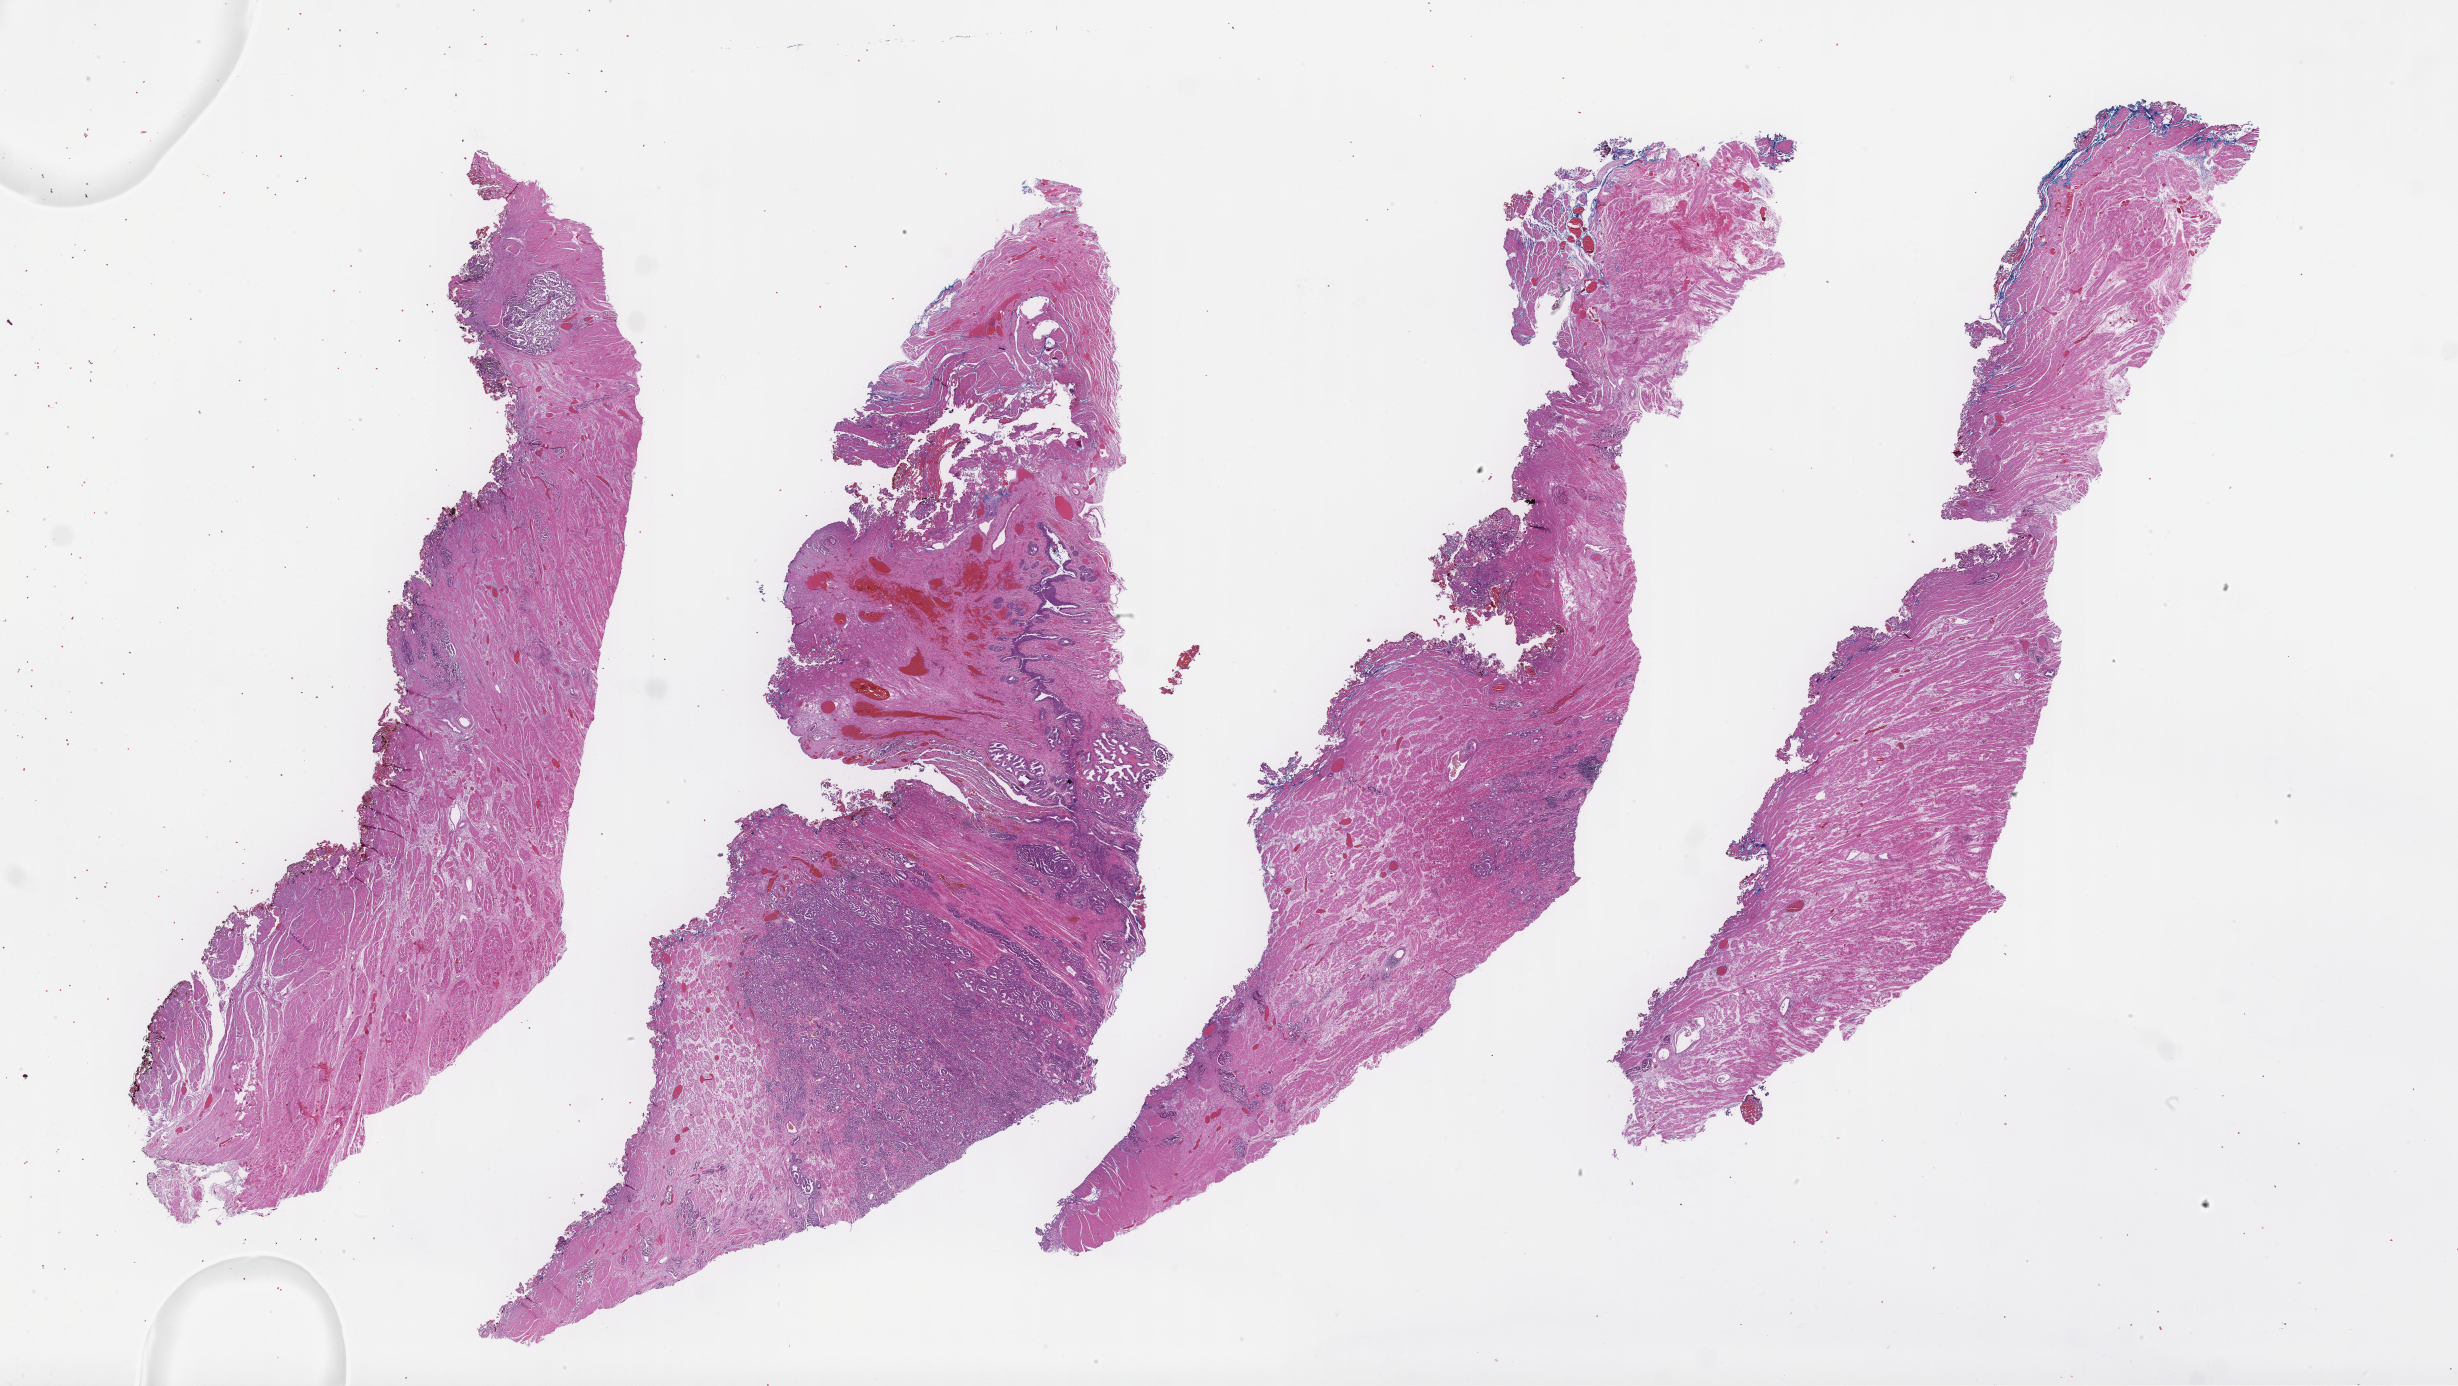
Digitized hematoxylin and eosin (H&E)-stained section, a low-resolution overview of the entire scanned area, about 39.7 x 22.4 mm; formalin-fixed, paraffin-embedded (FFPE) tissue; tissue site: prostate; specimen time point: archival tissue. Patient sex: male.
This section: primary tumour tissue. Diagnosis: Prostate Carcinoma.